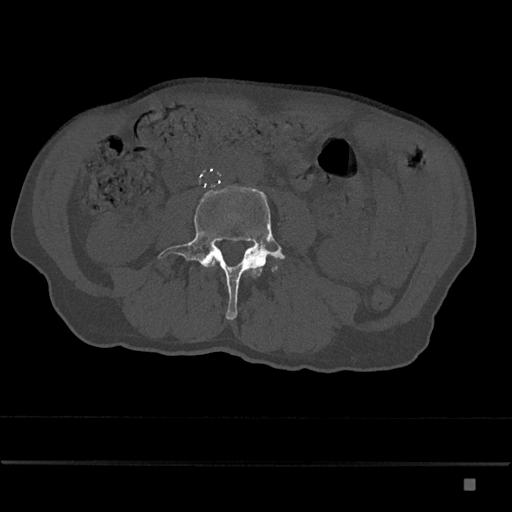
CT including the spine, one axial slice. Position 347 of 797 along the scan axis. 120 kVp. Bone window (W 1800 / L 400 HU). 0.5 mm slice thickness. 512 × 512 image matrix. Patient: male, 72 years. Case-level facts recorded for this patient, not image findings: primary cancer: prostate.
Outlined on this slice (semi-automatically segmented with operator editing):
- L3 vertebra: box from (x=208, y=258) to (x=217, y=268) px
- L4 vertebra: (x=158, y=186)–(x=286, y=320)